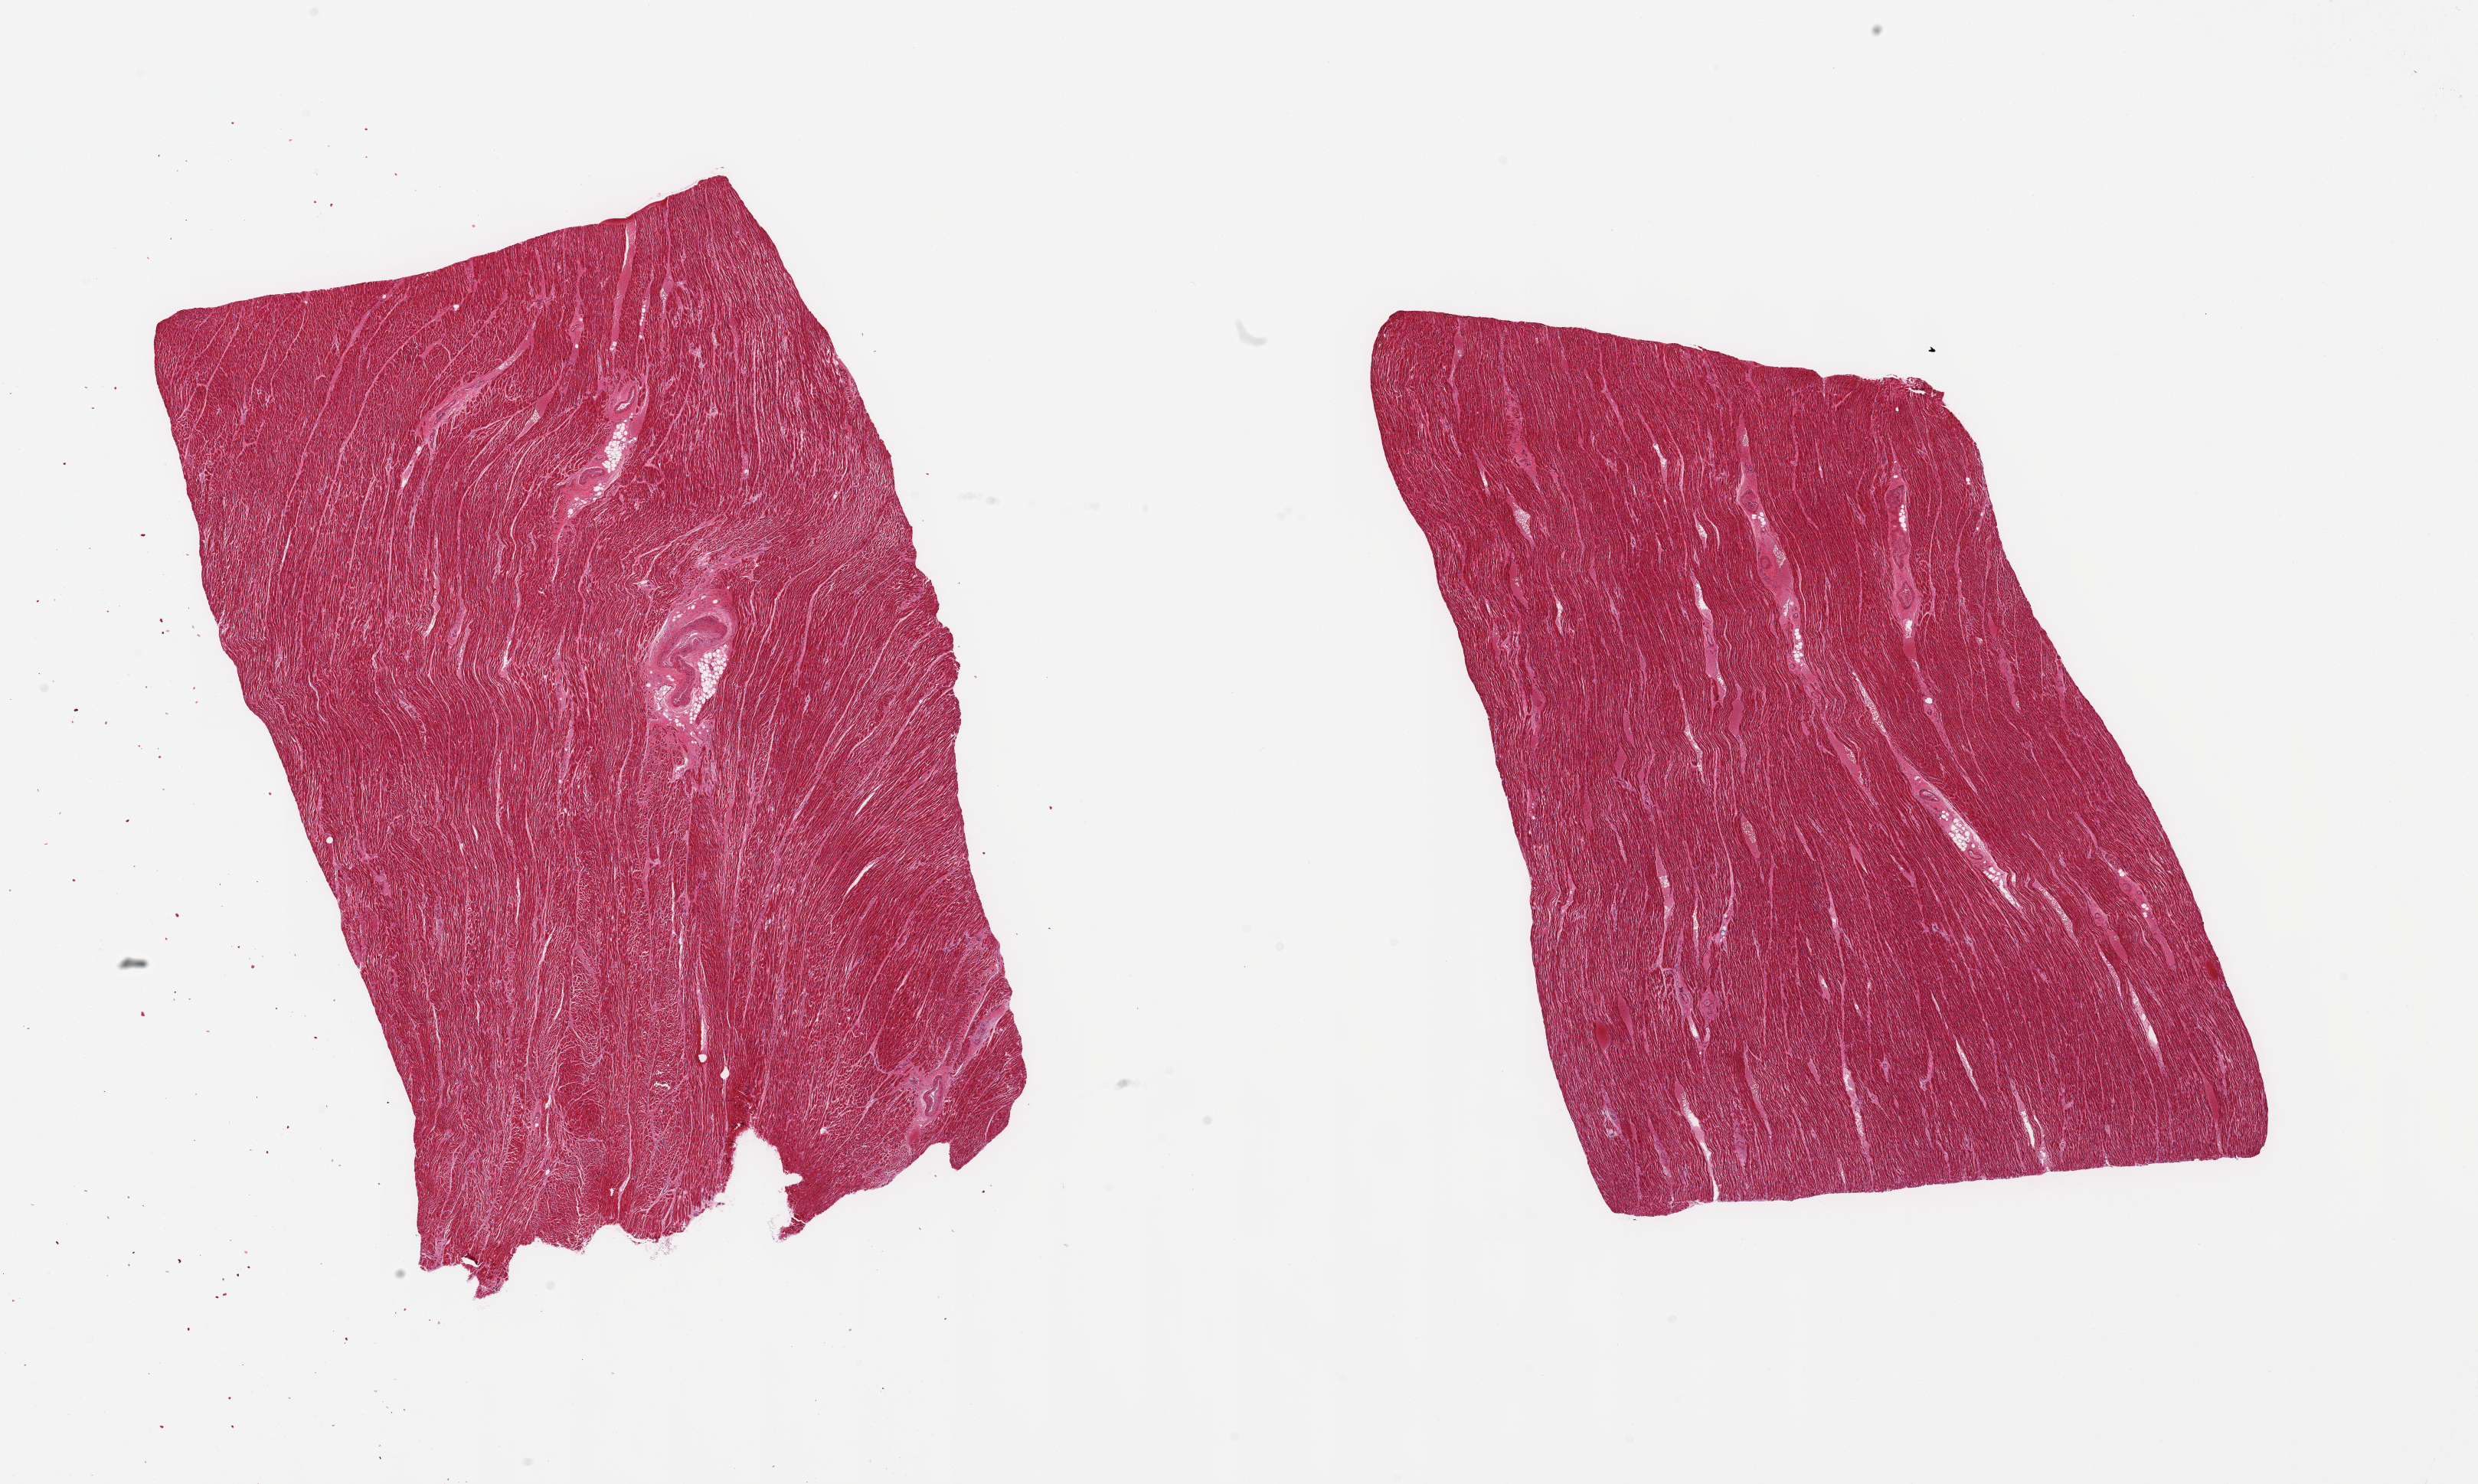
Hematoxylin and eosin (H&E) whole-slide image, brightfield, whole scanned area (about 25.6 x 15.3 mm) shown as a low-resolution overview; PAXgene-fixed, paraffin-embedded tissue; sampled site (target tissue): heart; tissue donor sample. Donor sex: male.
* pathologist's review note for this sample: 2 piece; moderately dilated congested blood vessels